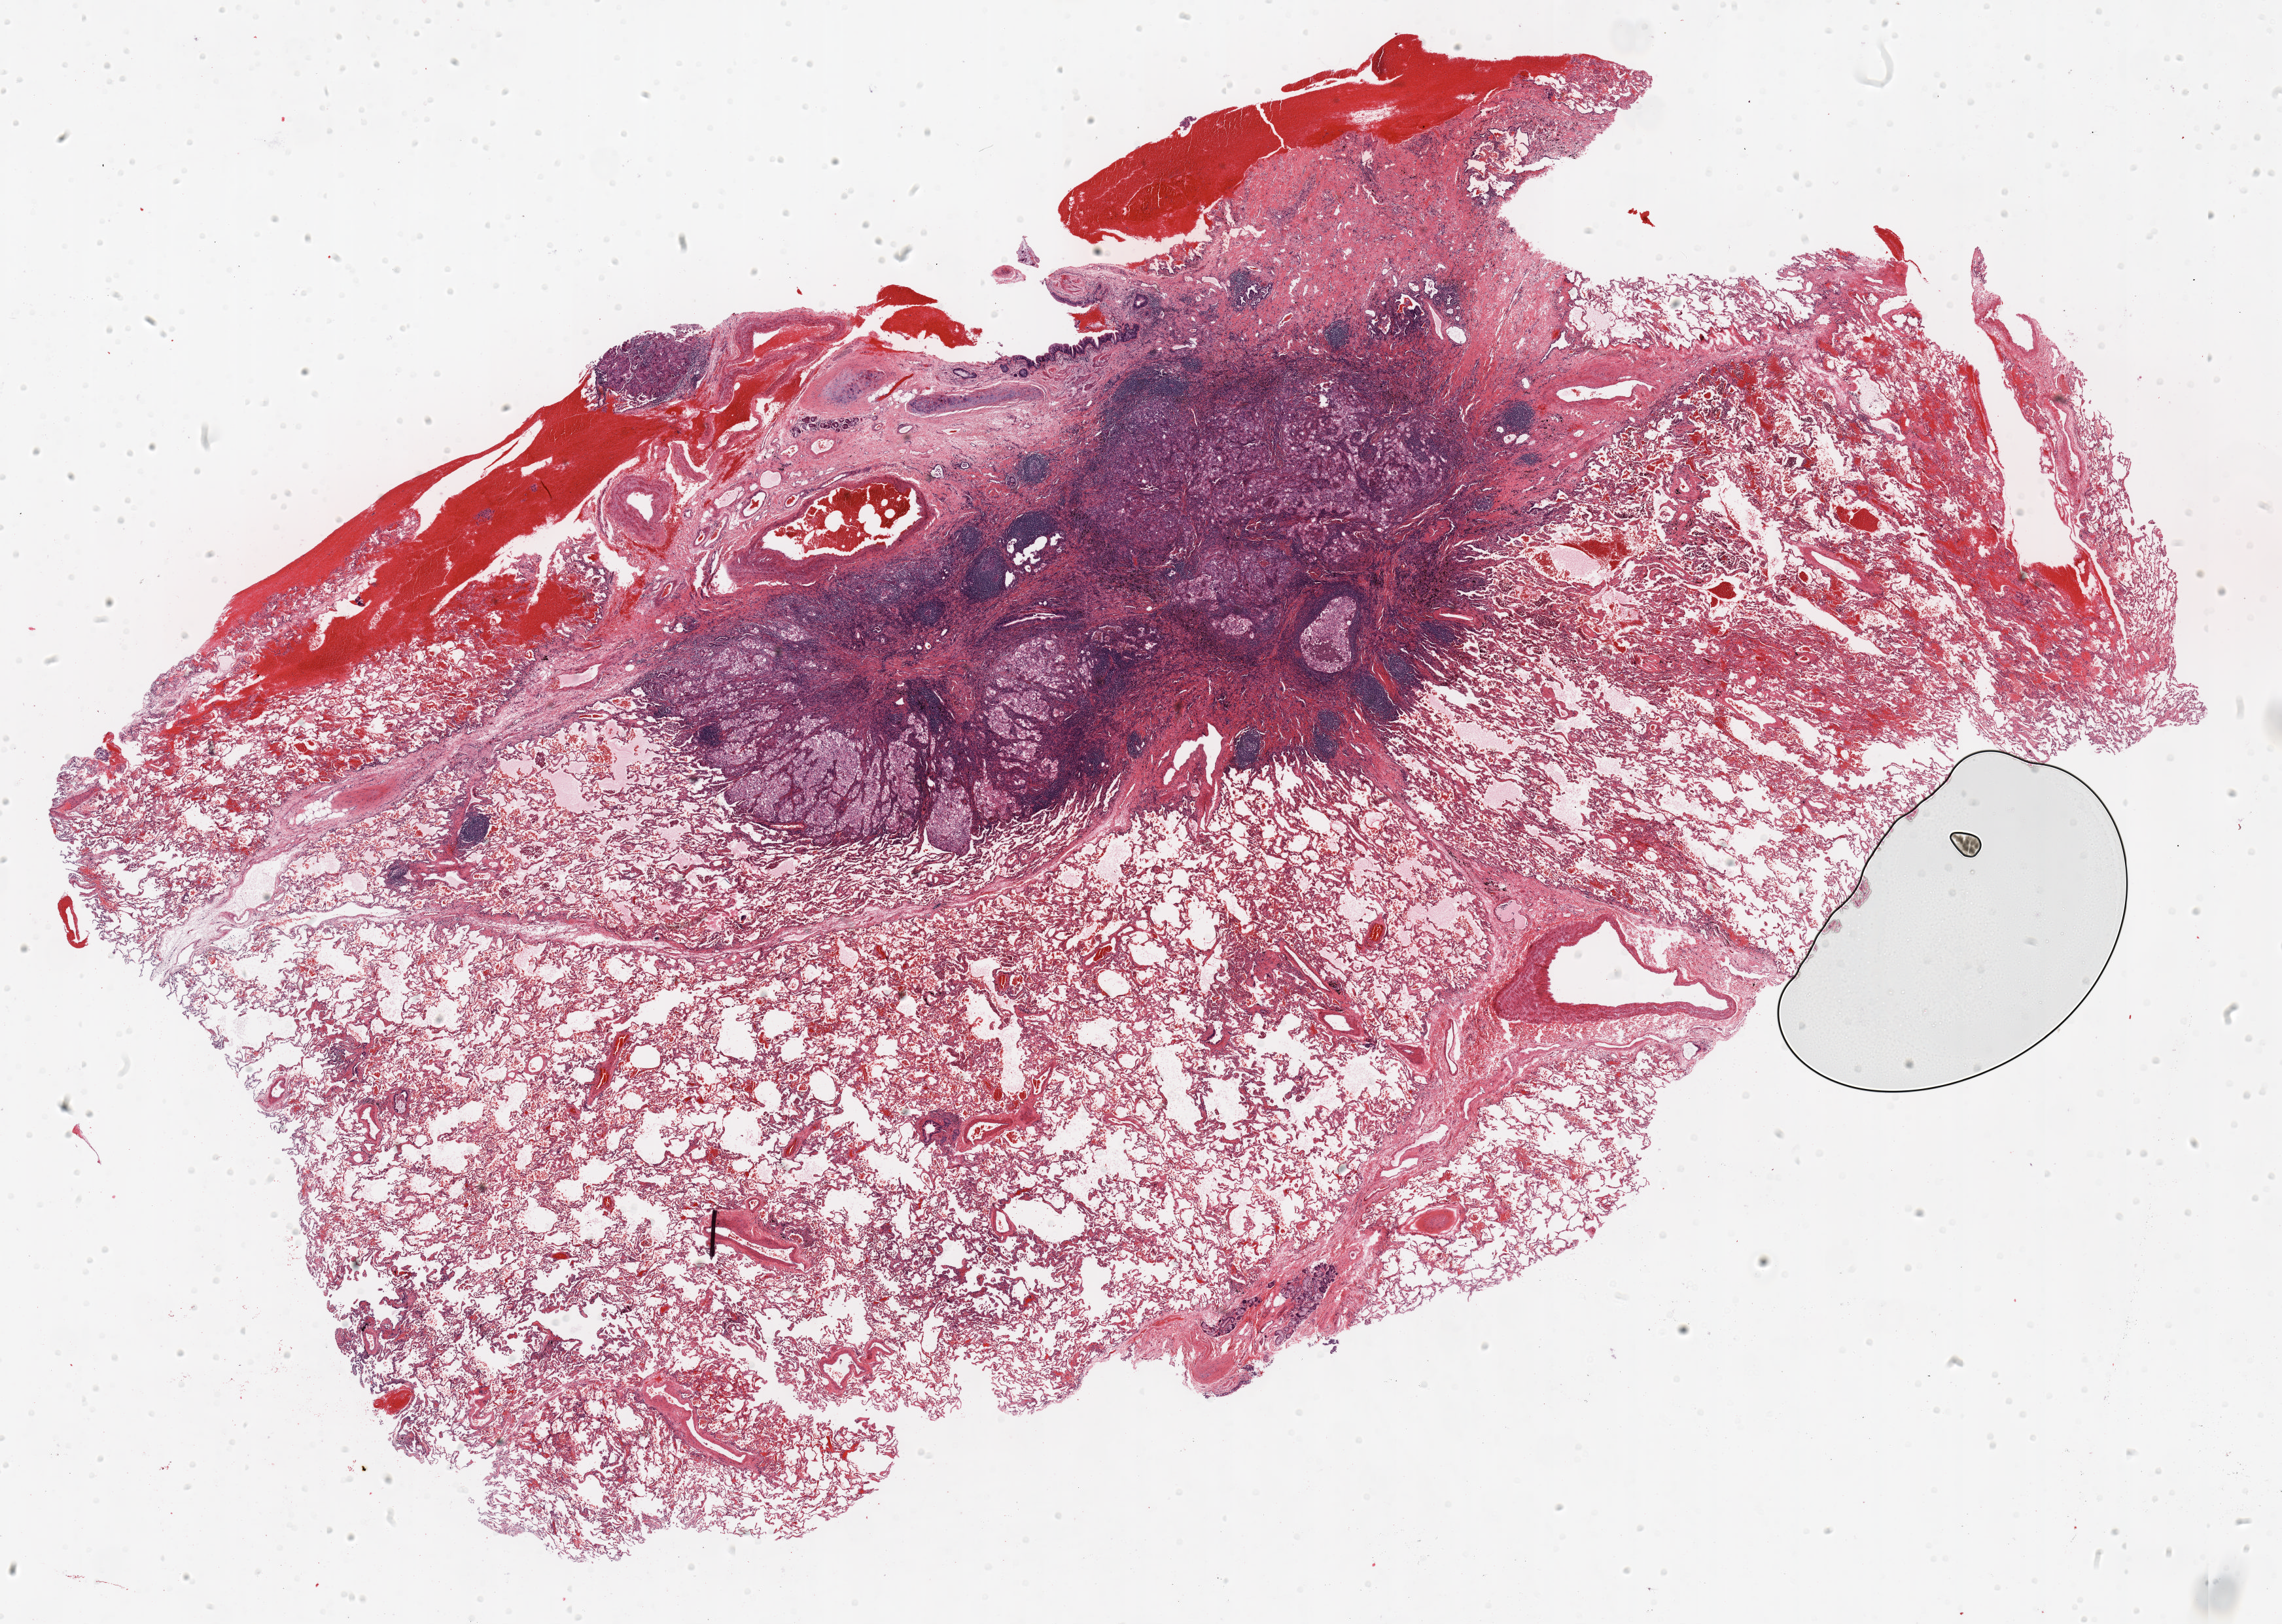
Whole-slide histology image, H&E — shown as a low-resolution overview of the whole scanned area (about 28.0 x 20.0 mm, slide scanned at 20x), FFPE section, lung tissue. Female, age 65 at enrolment. Current smoker at enrolment.
Participant's lung-cancer diagnosis: Large cell carcinoma, NOS (ICD-O-3 8012/3).